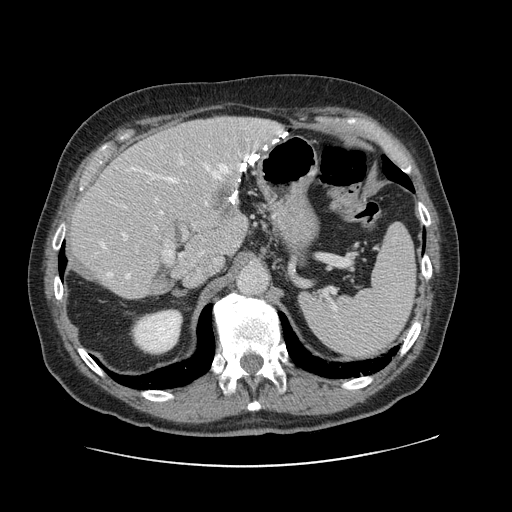
Contrast-enhanced abdominal CT, one axial slice; position 78 of 138 along the scan axis; intravenous contrast given; soft-tissue window (W 400 / L 40 HU); 2.5 mm slice thickness; 512 × 512 image matrix, field of view 402 × 402 mm. Male patient, age 71 years. From the clinical record (not read from this slice): diagnosis: colorectal cancer liver metastases, imaged before liver resection; multiple liver metastases: no; largest metastasis: 3.3 cm; chemotherapy before resection: no.
Structures marked on this image (outlined manually by an expert reader):
- hepatic veins: bounding box (x1, y1, x2, y2) in pixels: (101, 146, 266, 279)
- liver: (71, 118, 282, 299)
- planned liver remnant (the part of the liver to remain after resection): (70, 150, 235, 299)
- portal vein (with intrahepatic branches): (121, 154, 185, 261)
- liver metastasis: (209, 183, 237, 219)